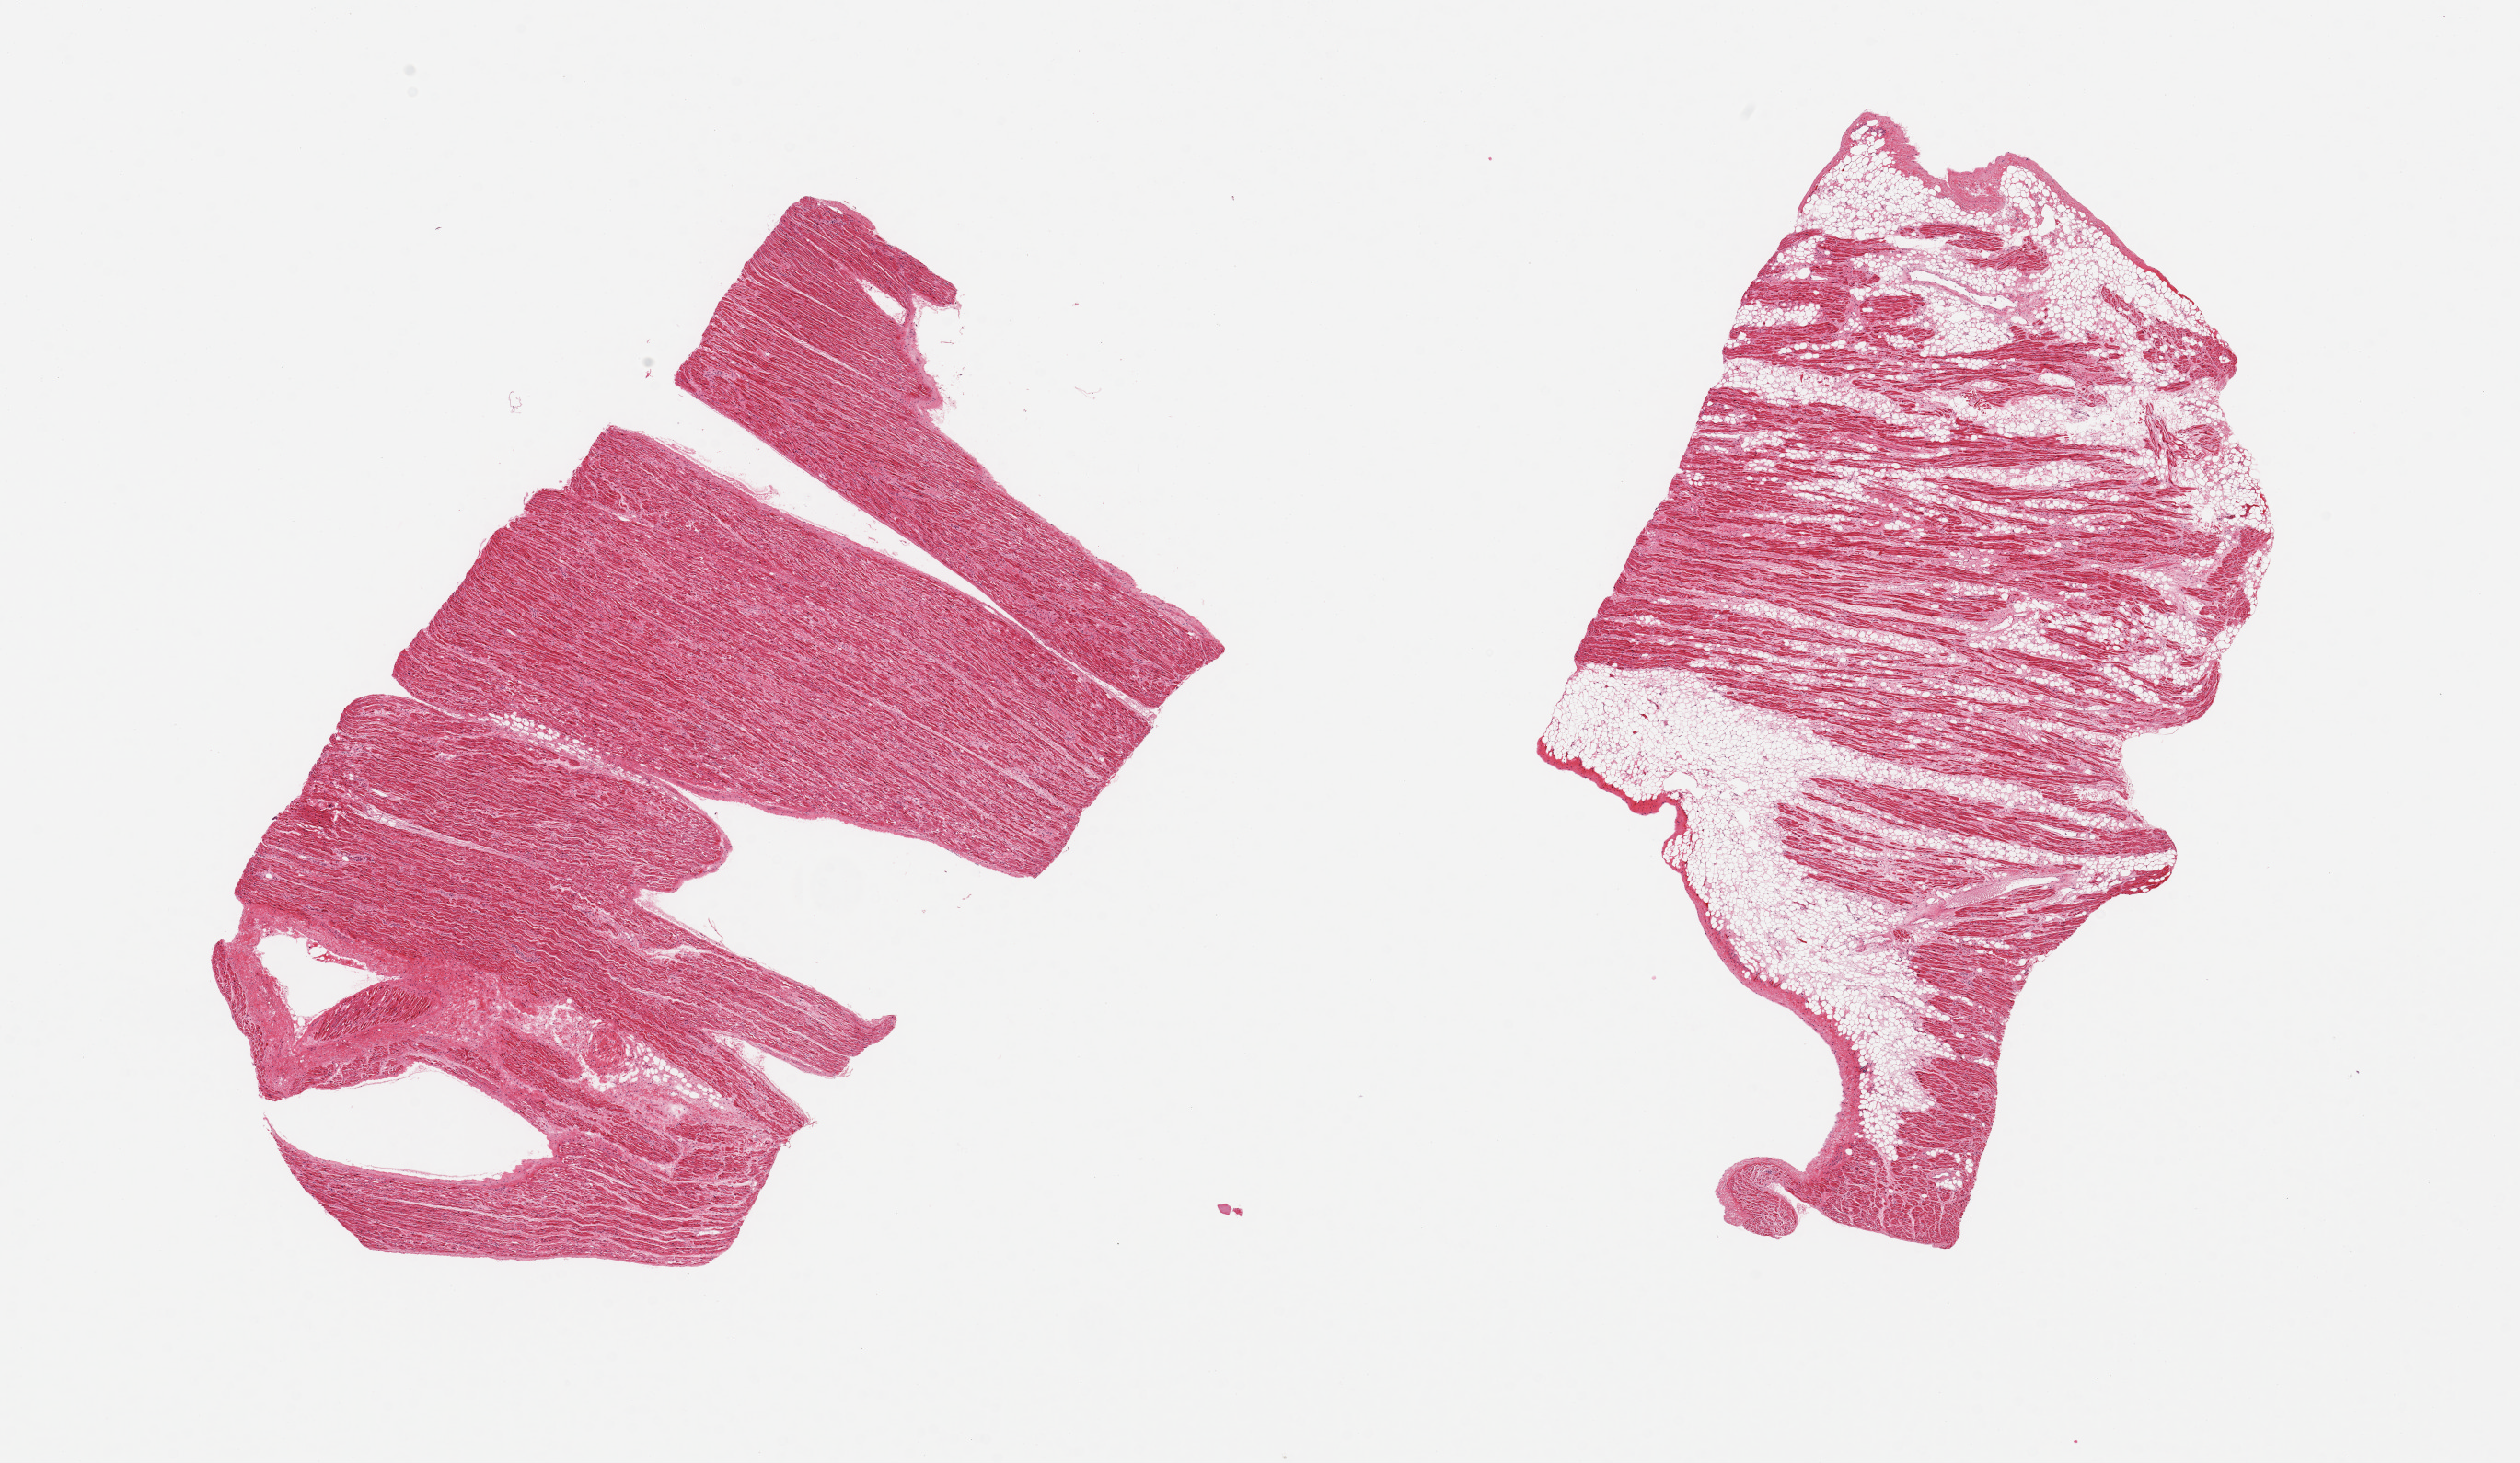
Digitized haematoxylin and eosin-stained section — shown as a low-resolution overview of the whole scanned area (about 21.7 x 12.6 mm, slide scanned at 20x). PAXgene-fixed paraffin-embedded (PFPE) section. Target tissue: auricular appendage. Tissue donor sample. Male donor.
Pathologist's review note for this sample: 2 pieces; one piece with ~60% internal fat and fibrosis.